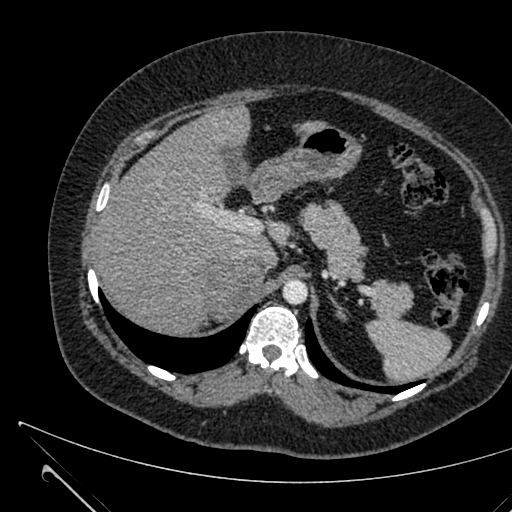
Contrast-enhanced abdominal CT, one axial slice; 120 kVp; intravenous contrast given; soft-tissue window (W 400 / L 40 HU); 512 × 512 image matrix, field of view 376 × 376 mm. Female patient, age 36 years. Case-level facts recorded for this patient, not image findings: diagnosis: adrenocortical carcinoma; tumour side: right adrenal; tumour size at pathology: 10 cm; Ki-67 index: 20 %.
Outlined on this slice (semi-automatically segmented with operator editing):
- mass: bounding box (x1, y1, x2, y2) in pixels: (205, 264, 263, 321)